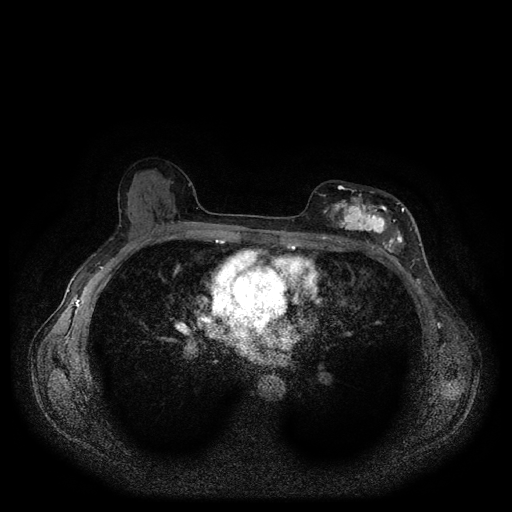
Breast MRI (dynamic contrast-enhanced, multi-phase), one axial slice. Slice 60 of 116 in the series (ordered by position). Dynamic contrast-enhanced series, time point 2 of 5 at this slice position (early post-contrast). 1.5 T. TE 2.6 ms, TR 5.3 ms. 2 mm slice thickness. 512 × 512 image matrix. Female patient, age 51 years.
Outlined on this slice (semi-automatically segmented with operator editing):
- breast lesion (labelled 'tumour' in the annotation; benign lesions carry a separate 'benign' label): bounding box <322,191,406,256> (left, top, right, bottom; pixels)